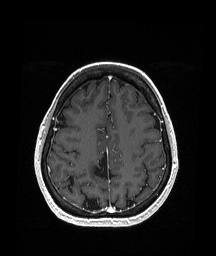
Brain MRI from a brain-tumour surgery series, one axial slice; position 62 of 151 along the scan axis; T1-weighted post-contrast; 1.05 mm slice thickness; 216 × 256 image matrix, field of view 211 × 250 mm. From the clinical record (not read from this slice): histopathology: Oligodendroglioma; WHO grade: 2; IDH mutation: yes.
Annotated regions visible in this slice (outlined manually by an expert reader):
- previous resection cavity: bounding box [x1, y1, x2, y2] px = [94, 149, 109, 183]